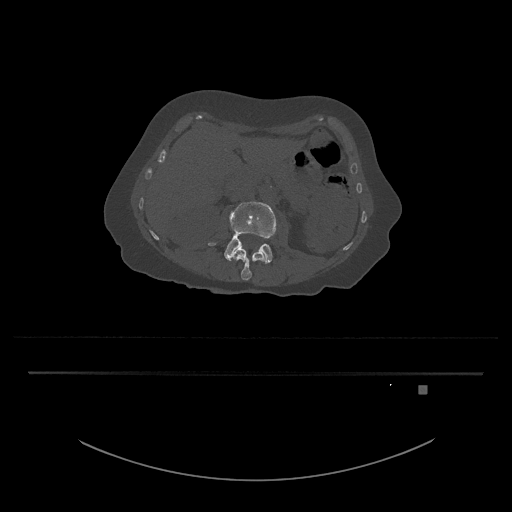
CT including the spine, one axial slice; slice 456 of 797 in the series (ordered by position); reconstruction kernel Br40s/3; 120 kVp; bone window (W 1800 / L 400 HU); 0.5 mm slice thickness; 512 × 512 image matrix. Female patient, age 57 years. Case-level facts recorded for this patient, not image findings: primary cancer: cervical.
Annotated regions visible in this slice (semi-automatic segmentation, software-assisted and operator-edited):
- L3 vertebra: bounding box (x1, y1, x2, y2) in pixels: (208, 201, 277, 264)